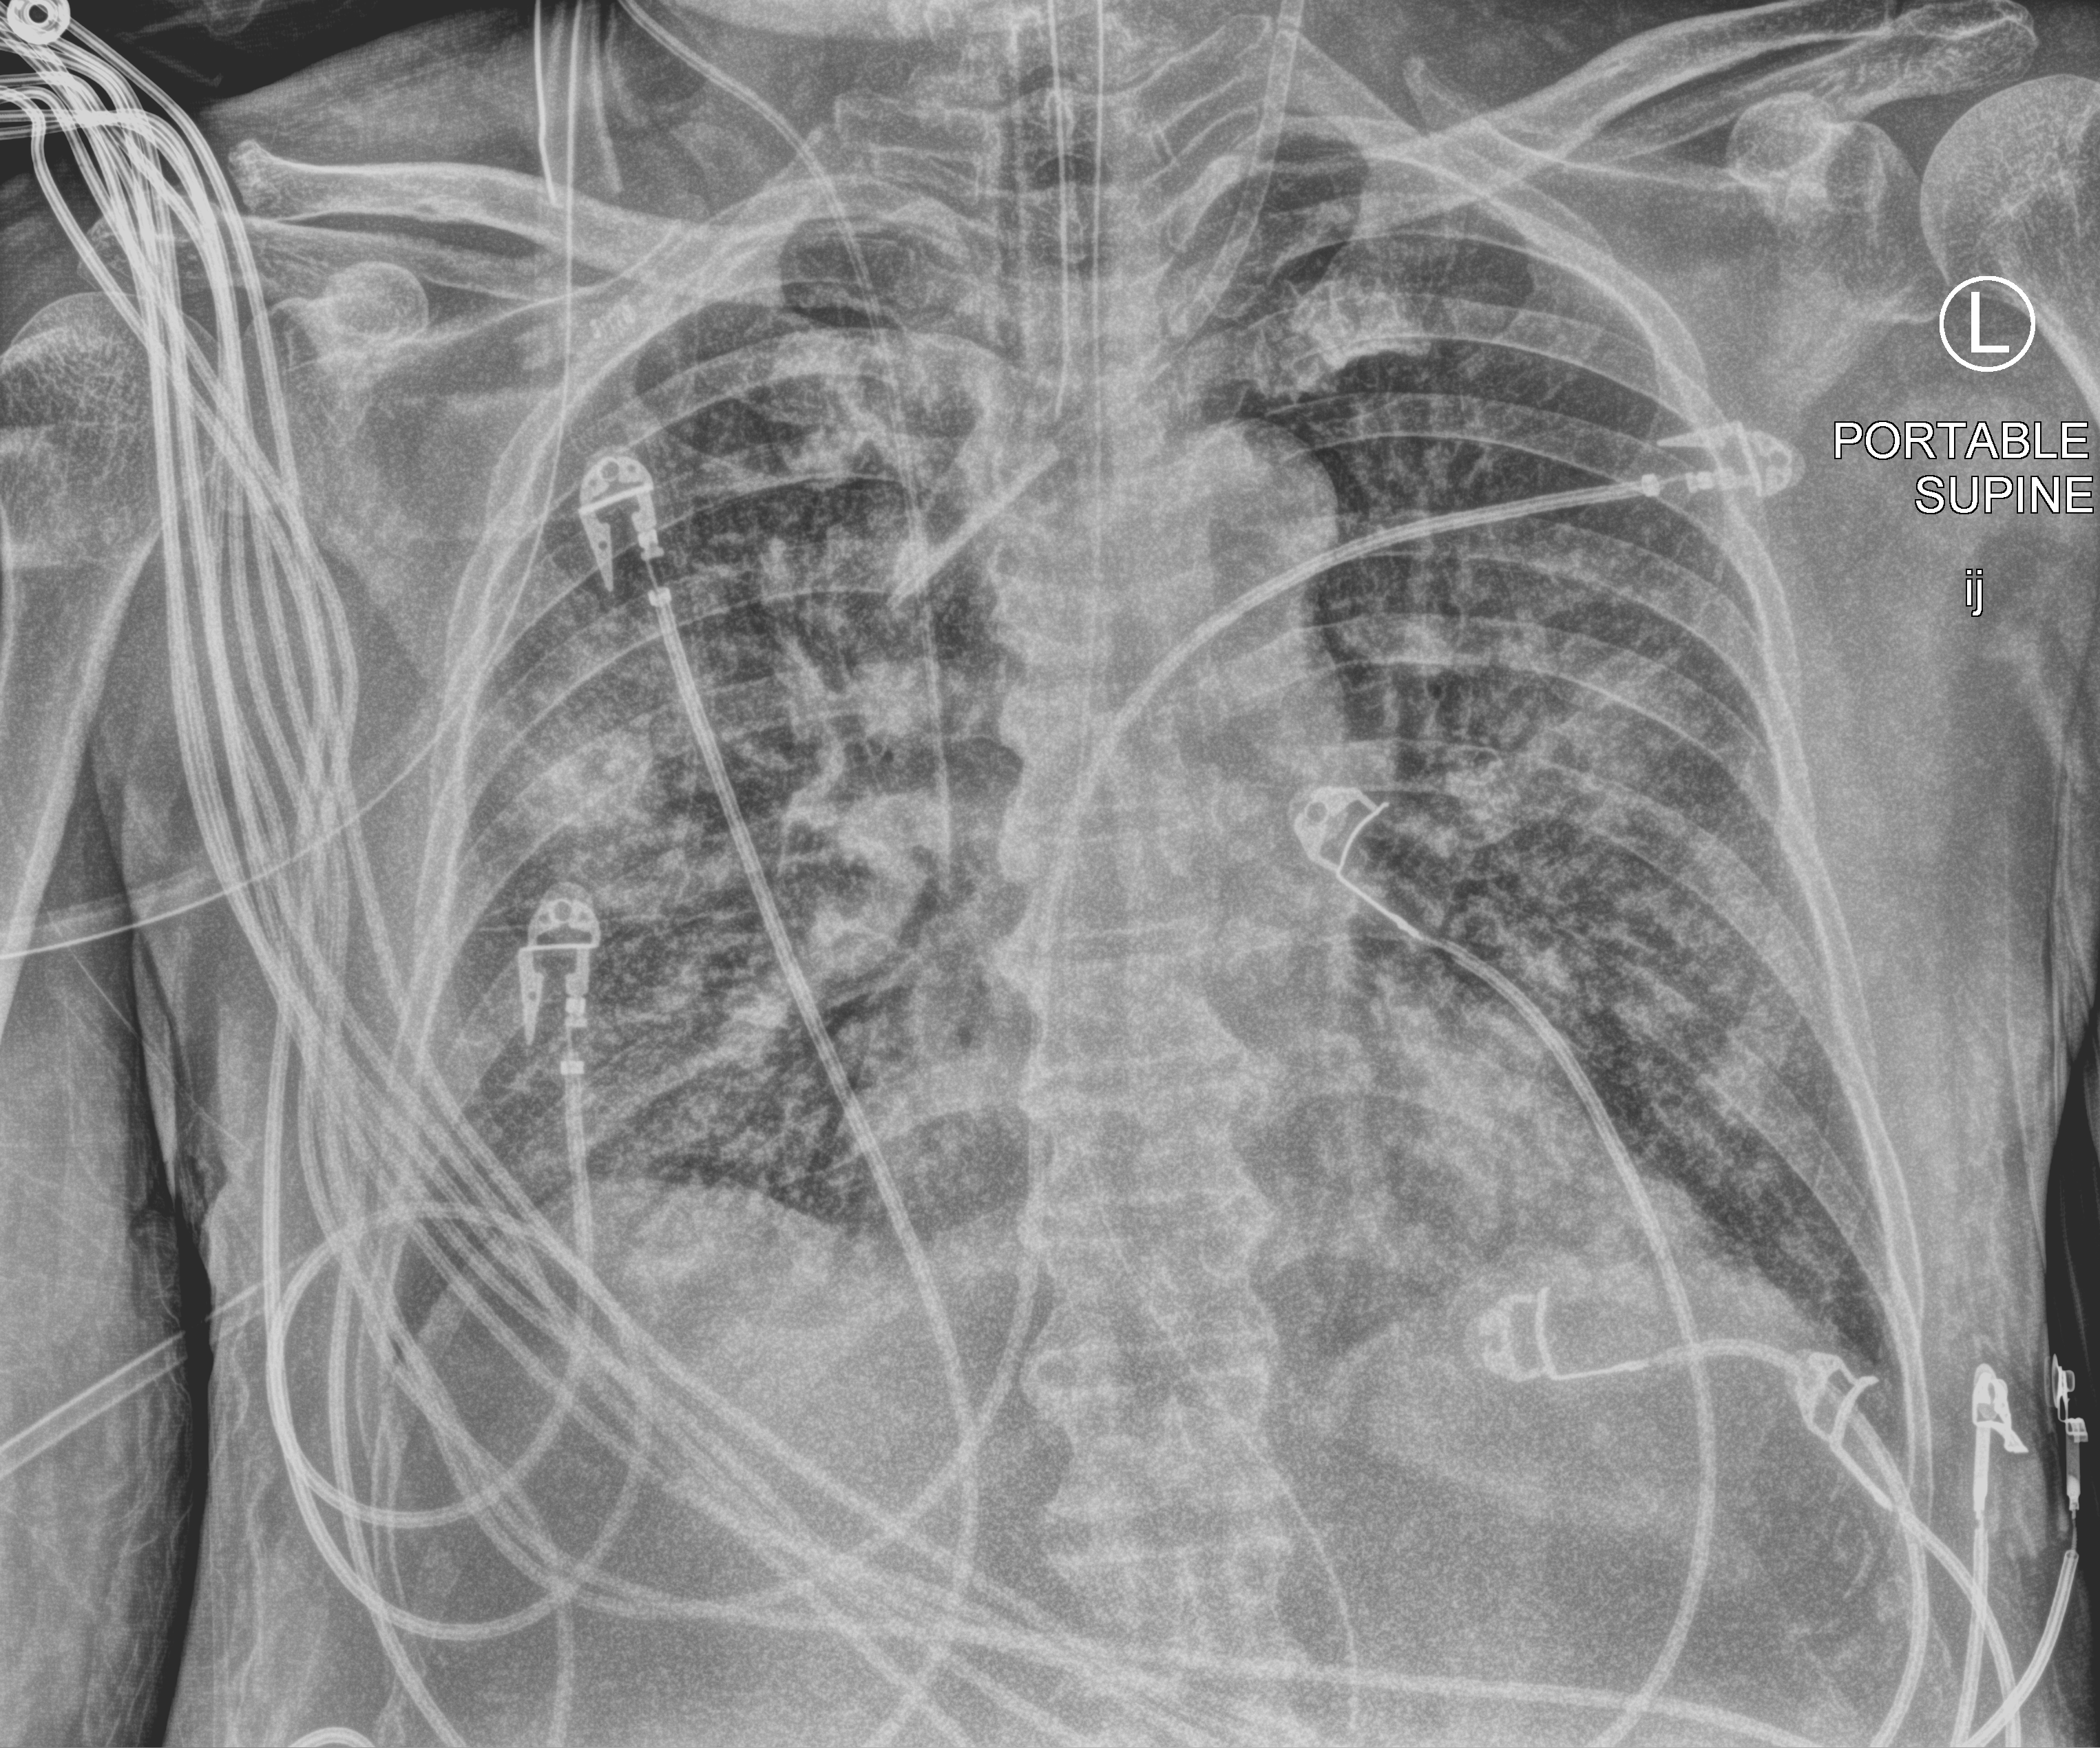
Portable chest radiograph; anteroposterior (AP) projection. Patient hospitalised with COVID-19; male, aged 60–74 years.
Hospital-stay facts (about this admission, not read from this image; timing relative to this image not recorded):
- admitted to intensive care during this hospital stay: yes
- mechanically ventilated during this hospital stay: yes
- chronic kidney disease (admission record): no